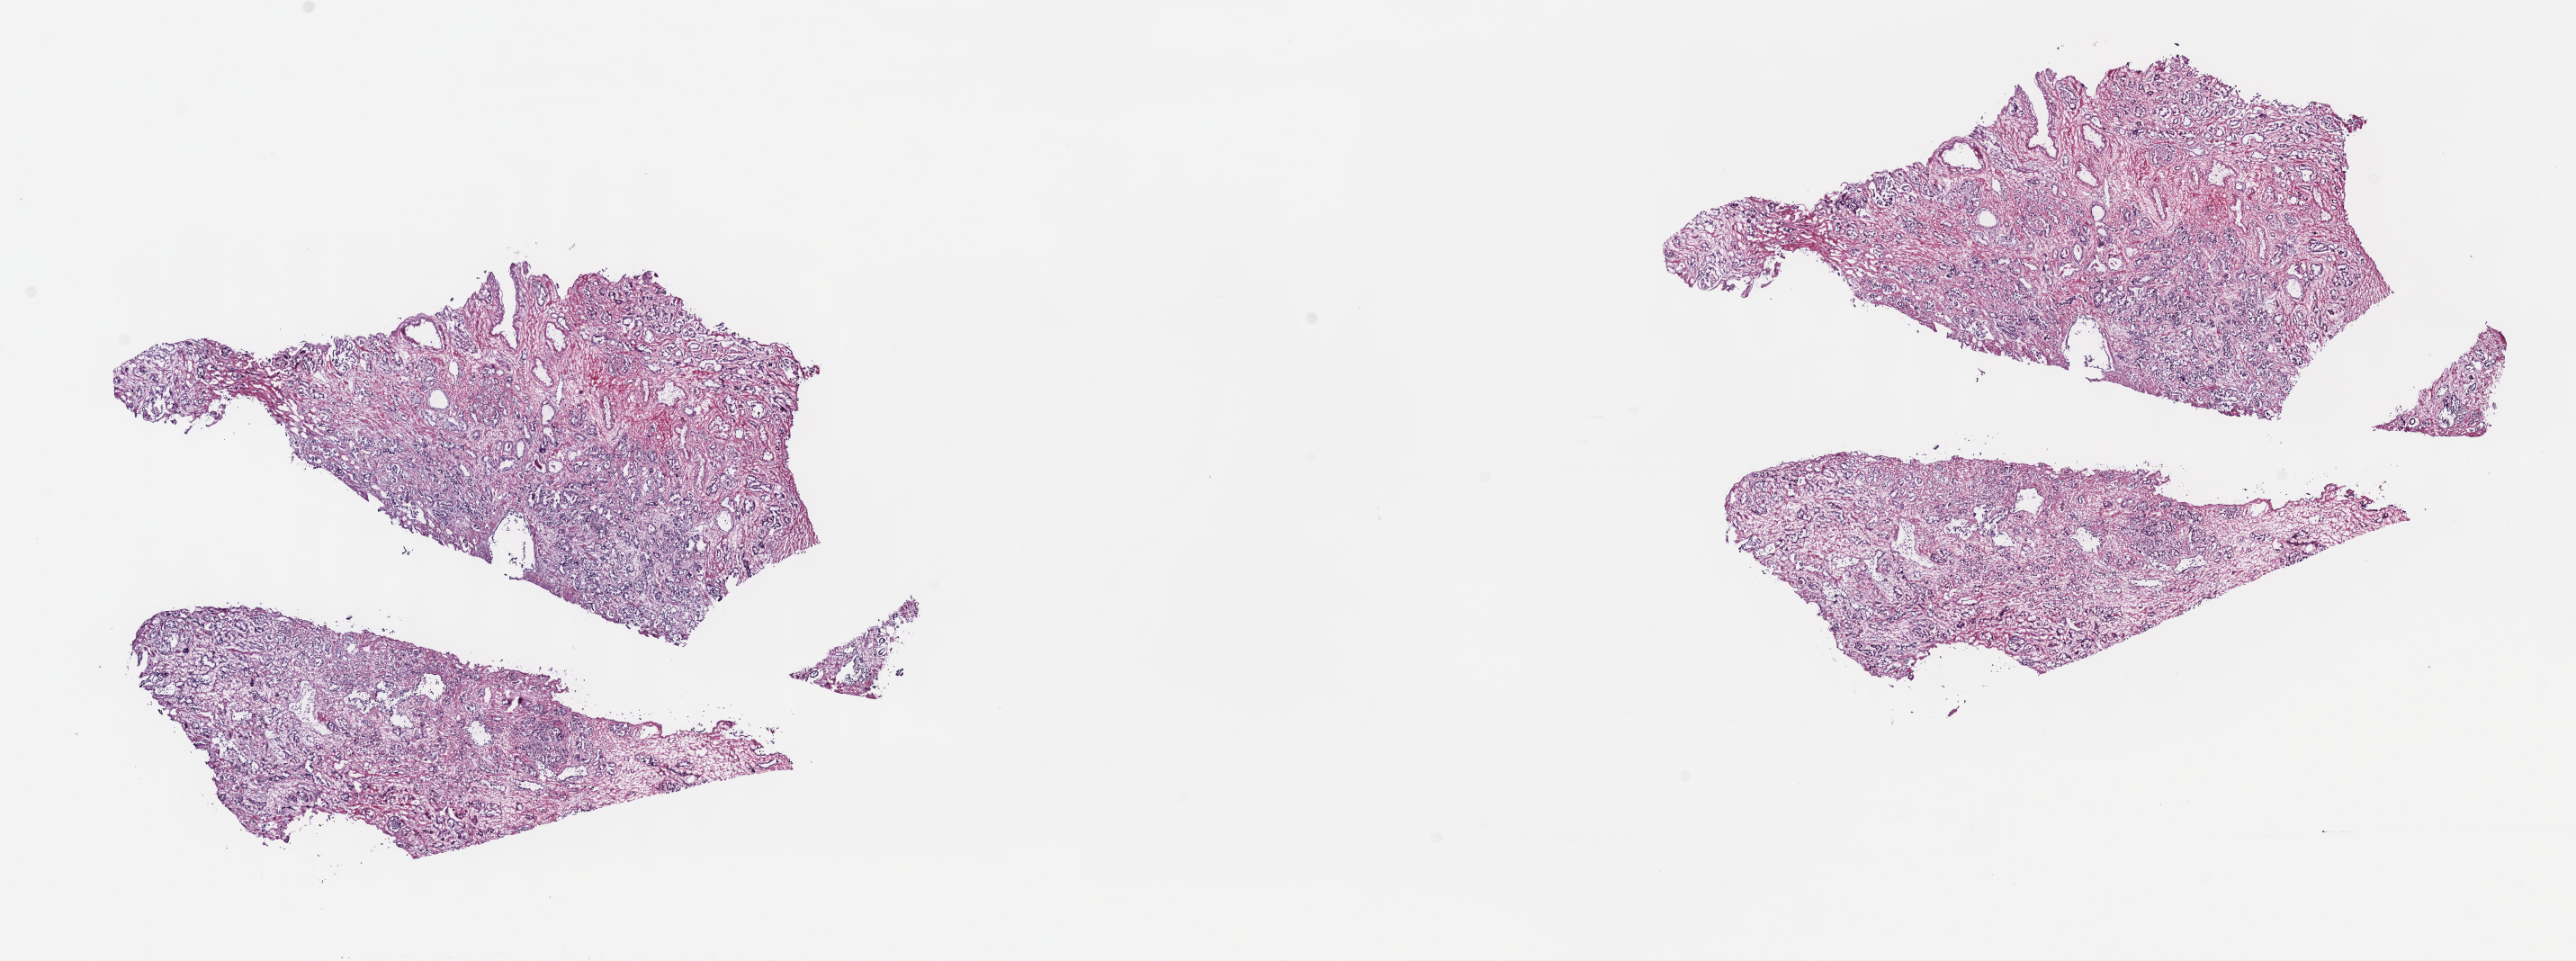
Digitized H&E-stained tissue section (whole slide), shown as a low-resolution overview of the whole scanned area (about 23.2 x 8.6 mm); frozen section from the top of the tissue portion; primary tumour sample from the prostate. Male, age 54 years at initial diagnosis. Gleason score: 7 (3+4). Composition of this section per pathologist review: tumour cells 80%, tumour nuclei 80%, normal cells 0%, stromal cells 20%, necrosis 0%. Infiltration values recorded for this section: lymphocyte infiltration 60%, monocyte infiltration 10%, neutrophil infiltration 20%.
* lymph nodes positive (case pathology): 0 of 18 examined
* diagnosis: Adenocarcinoma, NOS (prostate gland)